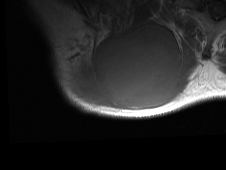
MRI of an extremity soft-tissue mass, one axial slice; position 51 of 81 along the scan axis; MR volume resampled by the dataset authors to the PET/CT grid (not the native acquisition matrix); 3.27 mm slice thickness; 226 × 170 image matrix, field of view 221 × 166 mm. Male patient. From the clinical record (not read from this slice): histological type: pleiomorphic spindle cell undifferentiated; grade: high; site of the primary tumour: right parascapusular.
Outlined on this slice (expert contour drawn on MRI and transferred to this co-registered scan by the dataset authors):
- gross tumour volume including surrounding oedema: bounding box <62,17,200,114> (left, top, right, bottom; pixels)
- gross tumour volume (mass): <67,24,182,110>